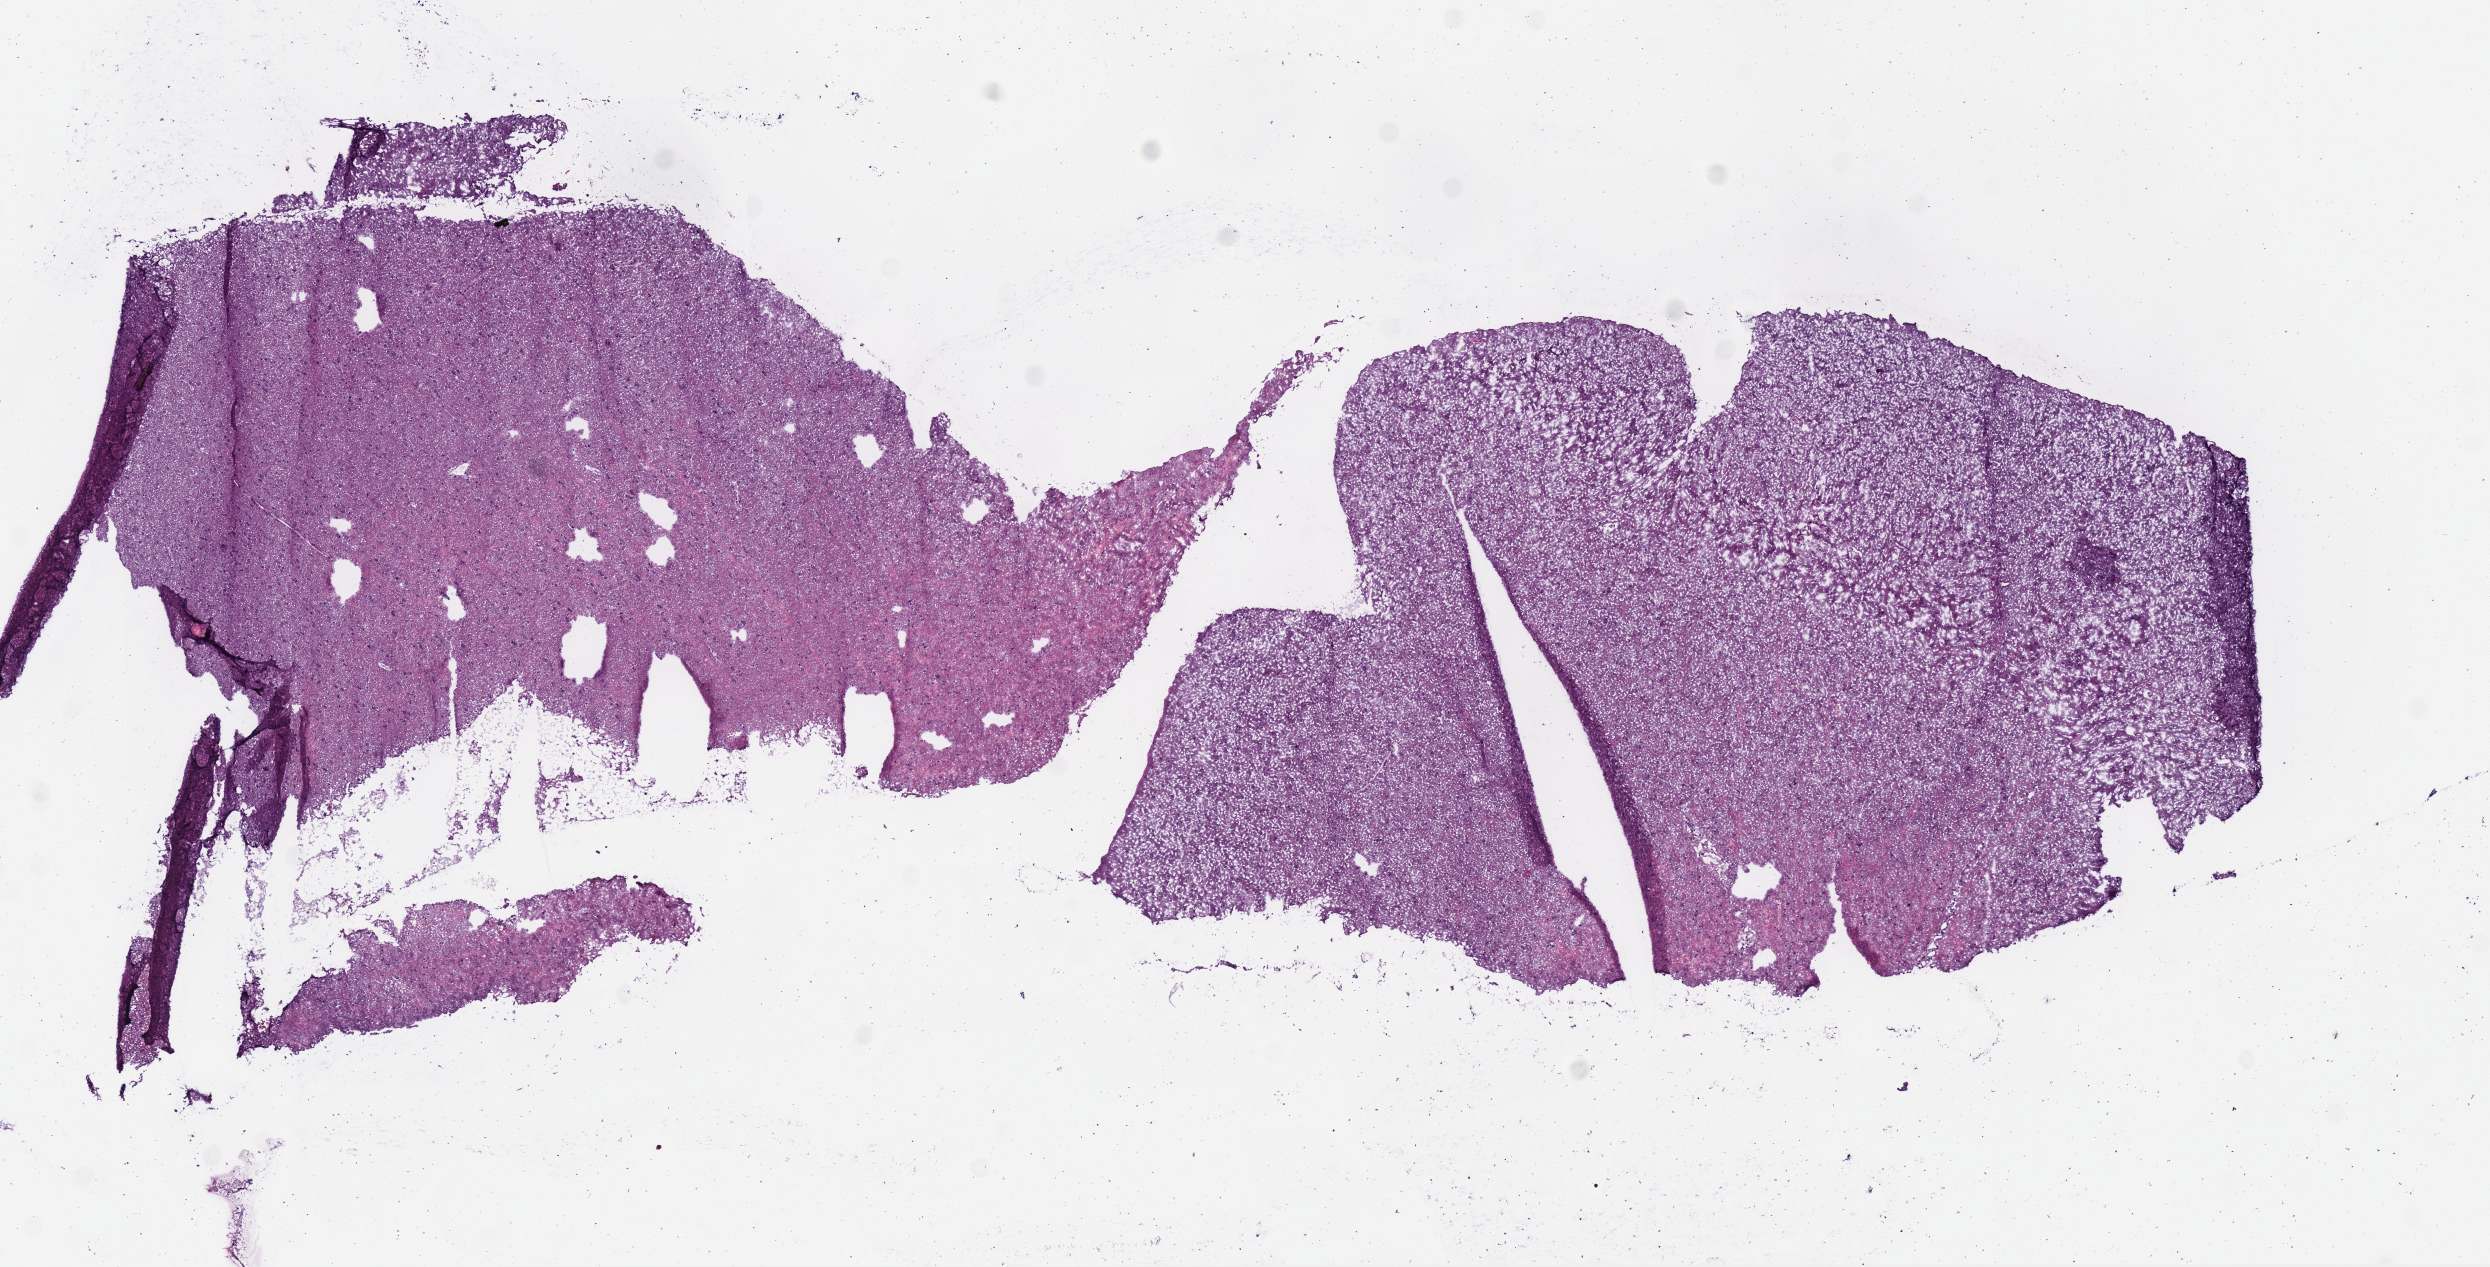
H&E-stained whole-slide image, low-resolution overview of the scanned area, about 9.8 x 5.0 mm (acquisition: 40x scan); frozen section from the bottom of the tissue portion; brain, primary tumour sample. Patient: male, age at initial diagnosis 62 years.
Pathologic diagnosis: Oligodendroglioma, NOS.